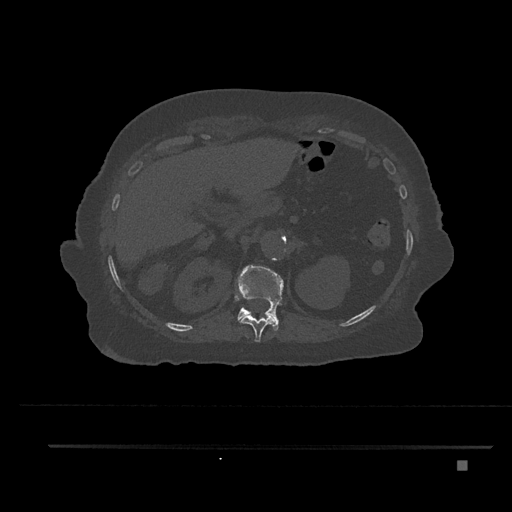
CT including the spine, one axial slice. Position 287 of 797 along the scan axis. Reconstruction kernel Br40s/3. 120 kVp. Bone window (W 1800 / L 400 HU). 512 × 512 image matrix. Patient: female, 76 years. Case-level facts recorded for this patient, not image findings: primary cancer: lung; vertebrae with lytic lesions (as recorded): T11, L3.
Annotated regions visible in this slice (semi-automatically segmented with operator editing):
- T11 vertebra: bounding box (x1, y1, x2, y2) in pixels: (239, 314, 276, 342)
- T12 vertebra: (236, 265, 284, 331)